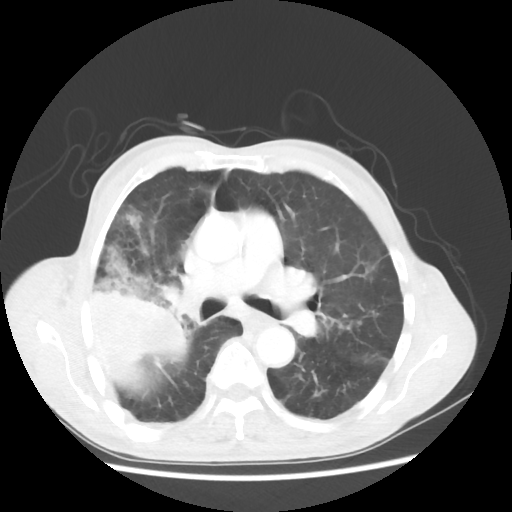
Chest CT, one axial slice. Position 33 of 58 along the scan axis. Lung window (W 1500 / L -600 HU). 5 mm slice thickness. 512 × 512 image matrix, field of view 351 × 351 mm. Patient: male, 75 years. From the clinical record (not read from this slice): clinical TNM (as recorded): T4 N1 M1.
Outlined on this slice (rectangle marked by the reading radiologist):
- lung tumour (recorded histology: adenocarcinoma): bounding box <85,253,195,399> (left, top, right, bottom; pixels)